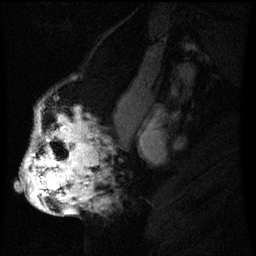
Breast MRI (dynamic contrast-enhanced), one sagittal slice. Slice 30 of 60 in the series (ordered by position). Dynamic contrast-enhanced series, image 2 of 3 at this slice position (ordered by acquisition). 1.5 T. TE 4.2 ms, TR 8 ms. 2.2 mm slice thickness. 256 × 256 image matrix, field of view 200 × 200 mm. Female patient, age 50 years.
Outlined on this slice (semi-automatically segmented with operator editing):
- analysis volume of interest (the breast-tissue region the enhancement analysis was run in; not a lesion): bounding box (x1, y1, x2, y2) in pixels: (24, 112, 109, 211)
- tumour enhancement mask (voxels above the 70 % enhancement threshold inside the analysis volume of interest): (25, 120, 93, 211)